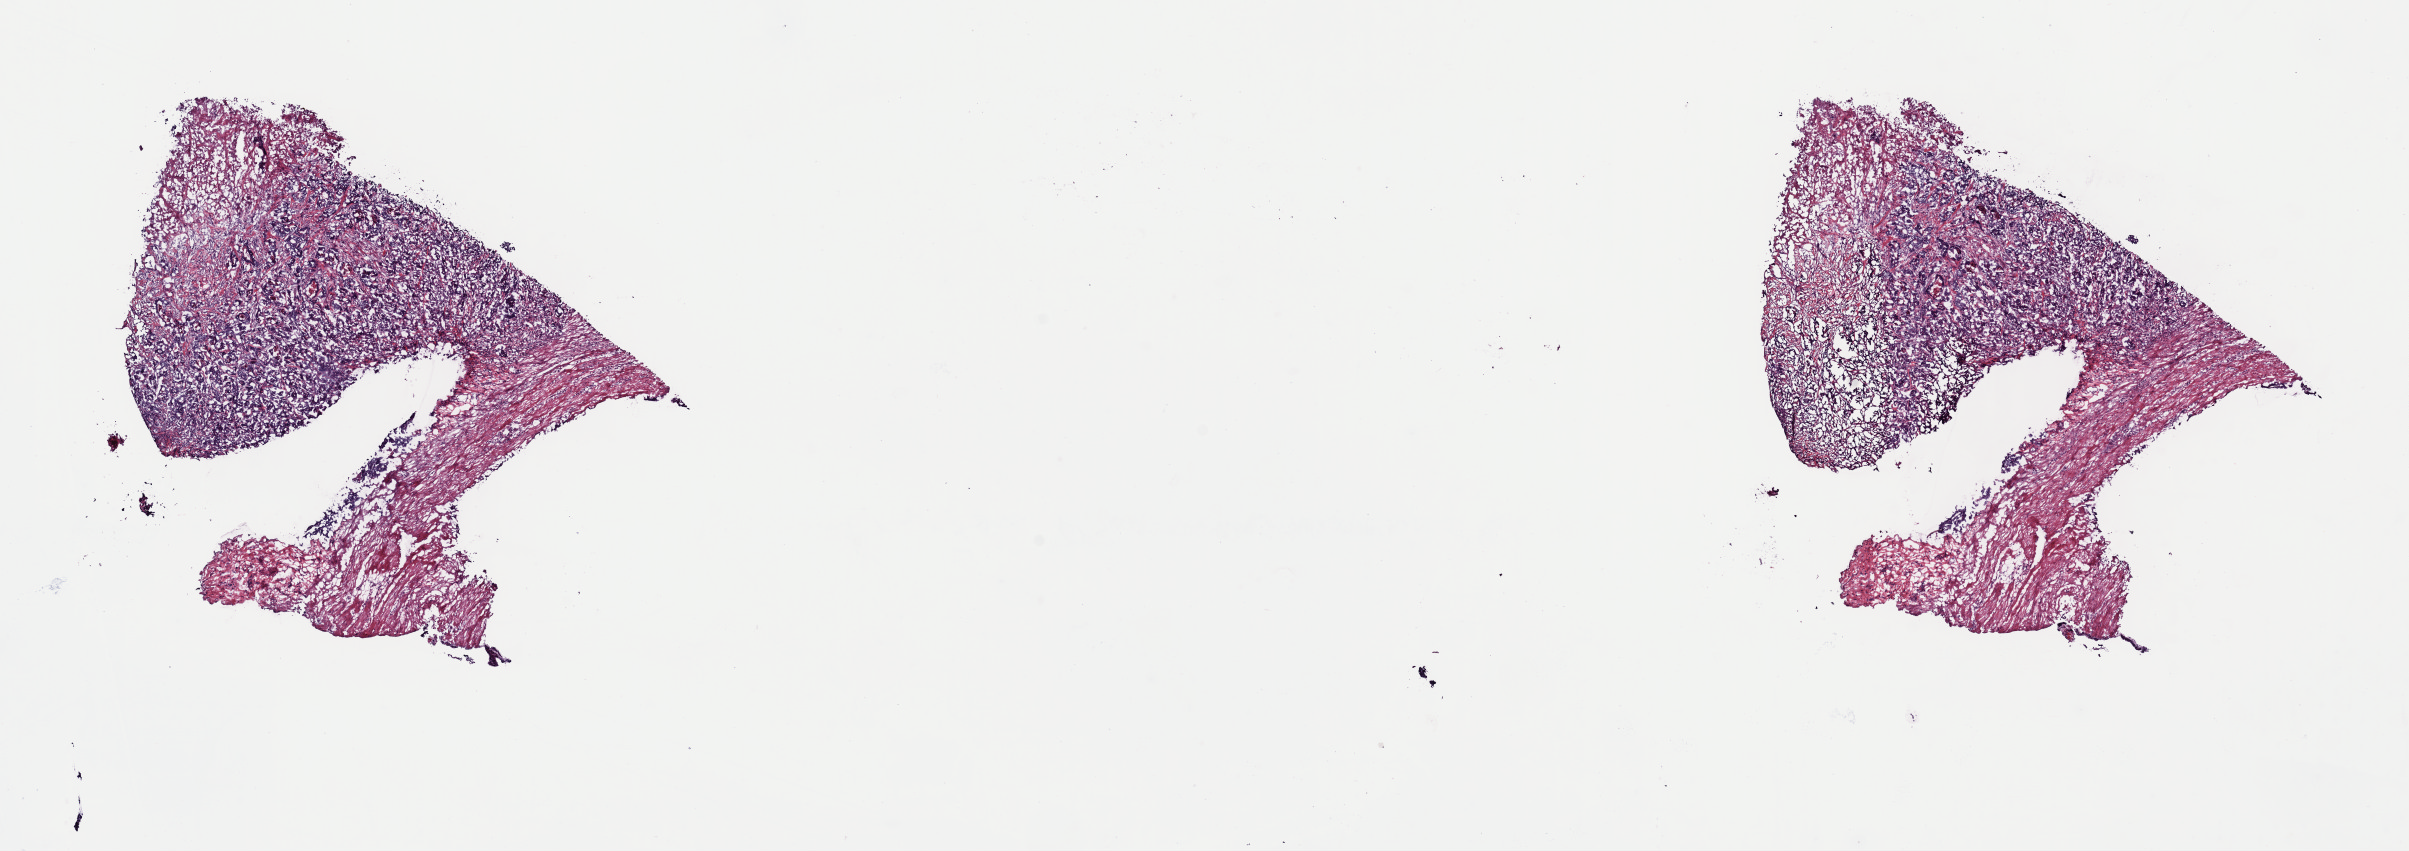
Whole-slide histology image, Hematoxylin and eosin (H&E) stained, shown as a low-resolution overview of the whole scanned area (about 19.0 x 6.7 mm, slide scanned at 40x), frozen section from the top of the tissue portion, sample: primary tumour, stomach. Male, age 71 years at initial diagnosis.
Pathologic diagnosis: Tubular adenocarcinoma (gastric antrum).